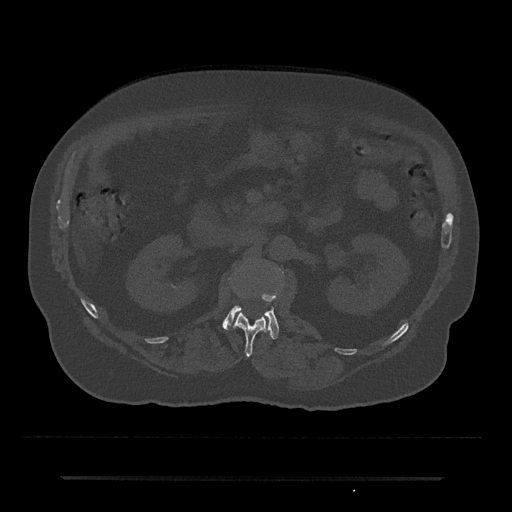
CT including the spine, one axial slice; slice 41 of 797 in the series (ordered by position); bone window (W 1800 / L 400 HU); 512 × 512 image matrix, field of view 437 × 437 mm. Male patient, age 69 years. Case-level facts recorded for this patient, not image findings: primary cancer: prostate.
Annotated regions visible in this slice (semi-automatically segmented with operator editing):
- L1 vertebra: bounding box [x1, y1, x2, y2] px = [228, 278, 268, 357]
- L2 vertebra: [222, 295, 279, 339]